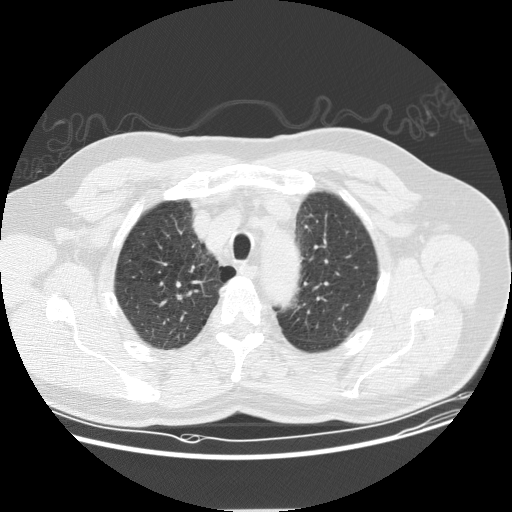
Low-dose screening chest CT, axial slice, first (baseline) screen, lung window (W 1500 / L -600 HU), 2.5 mm slice thickness, standard (soft-tissue) reconstruction kernel (STANDARD), slice 31 of 157 in the series. Male participant, aged 61 years at enrolment.
Expert-annotated lung lesion, box from (x=157, y=283) to (x=197, y=319) px. Screening reader's record for this exam: no non-calcified nodule ≥4 mm recorded. Official screen result: negative screen, minor abnormalities not suspicious for lung cancer. Later outcome: lung cancer diagnosed 832 days after this screen — squamous cell carcinoma, NOS, right upper lobe, moderately differentiated (G2), stage IA (AJCC 6th edition), 10 mm at pathology.